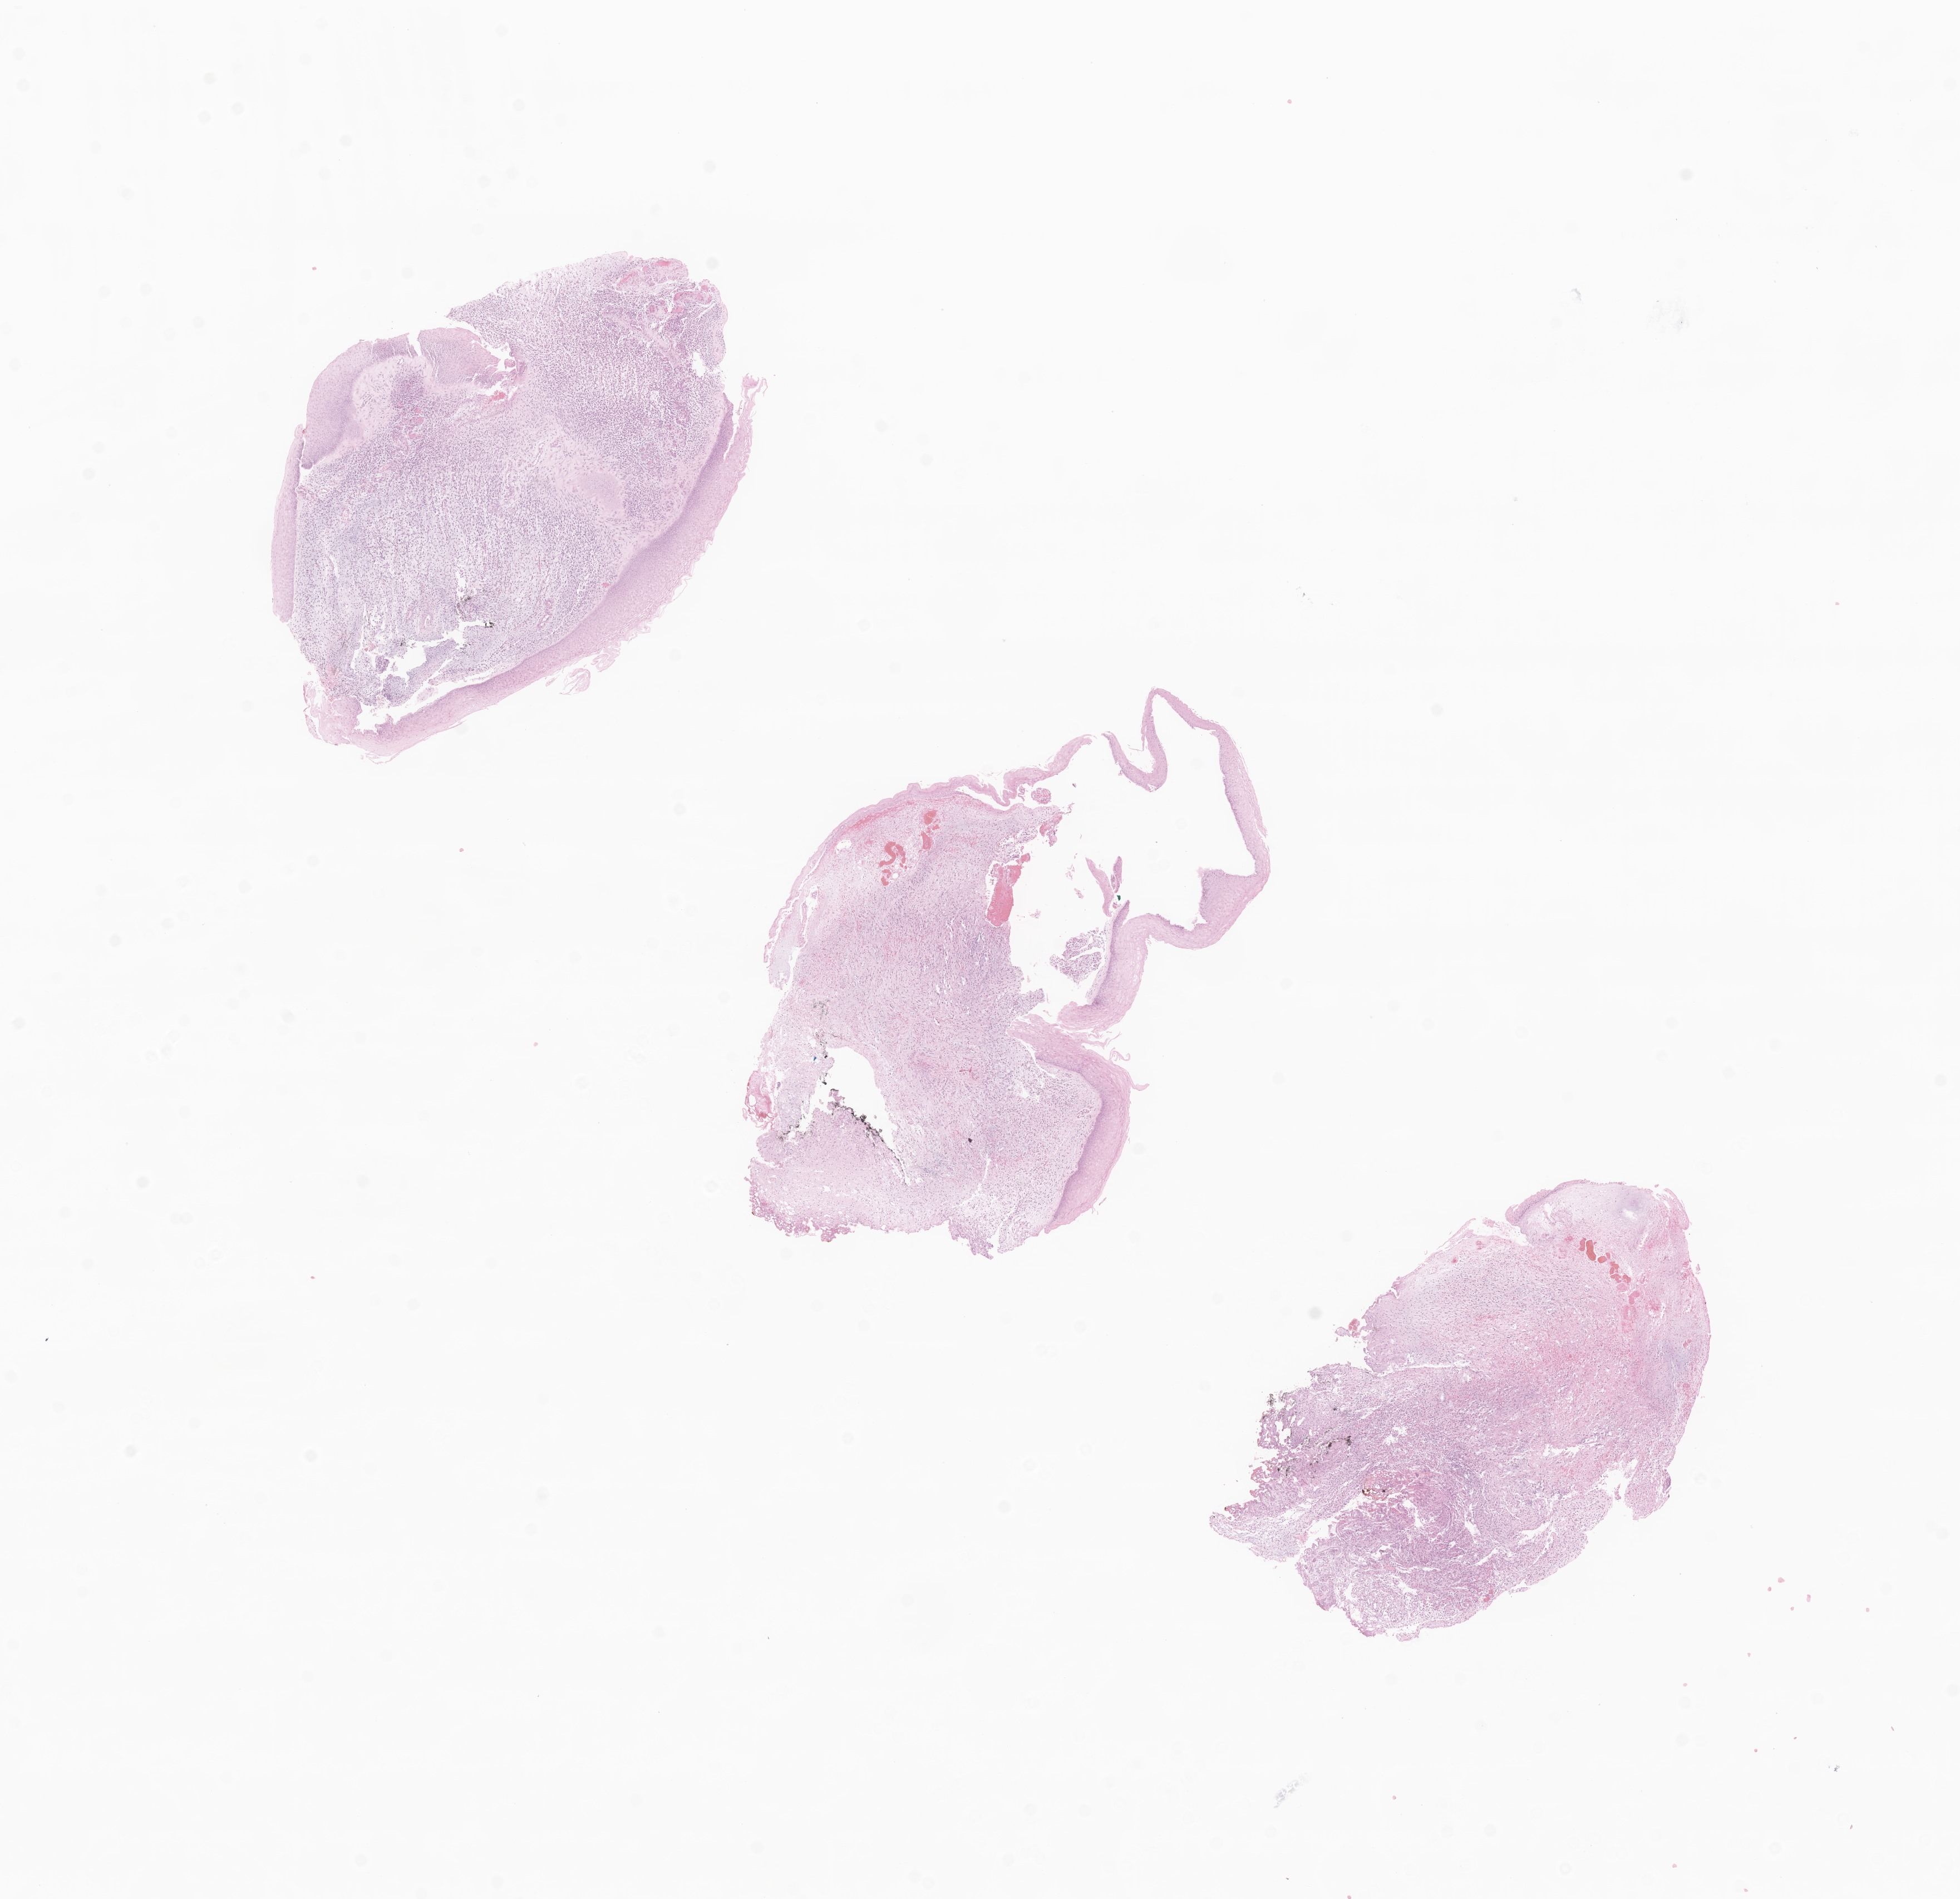
Digitized hematoxylin and eosin (H&E)-stained section of tumor tissue from the vagina, shown as a low-resolution overview of the whole scanned area (about 14.8 x 14.4 mm). FFPE section. Patient: female, age 904 days (about 2.5 years).
• recorded diagnosis: Embryonal rhabdomyosarcoma, NOS